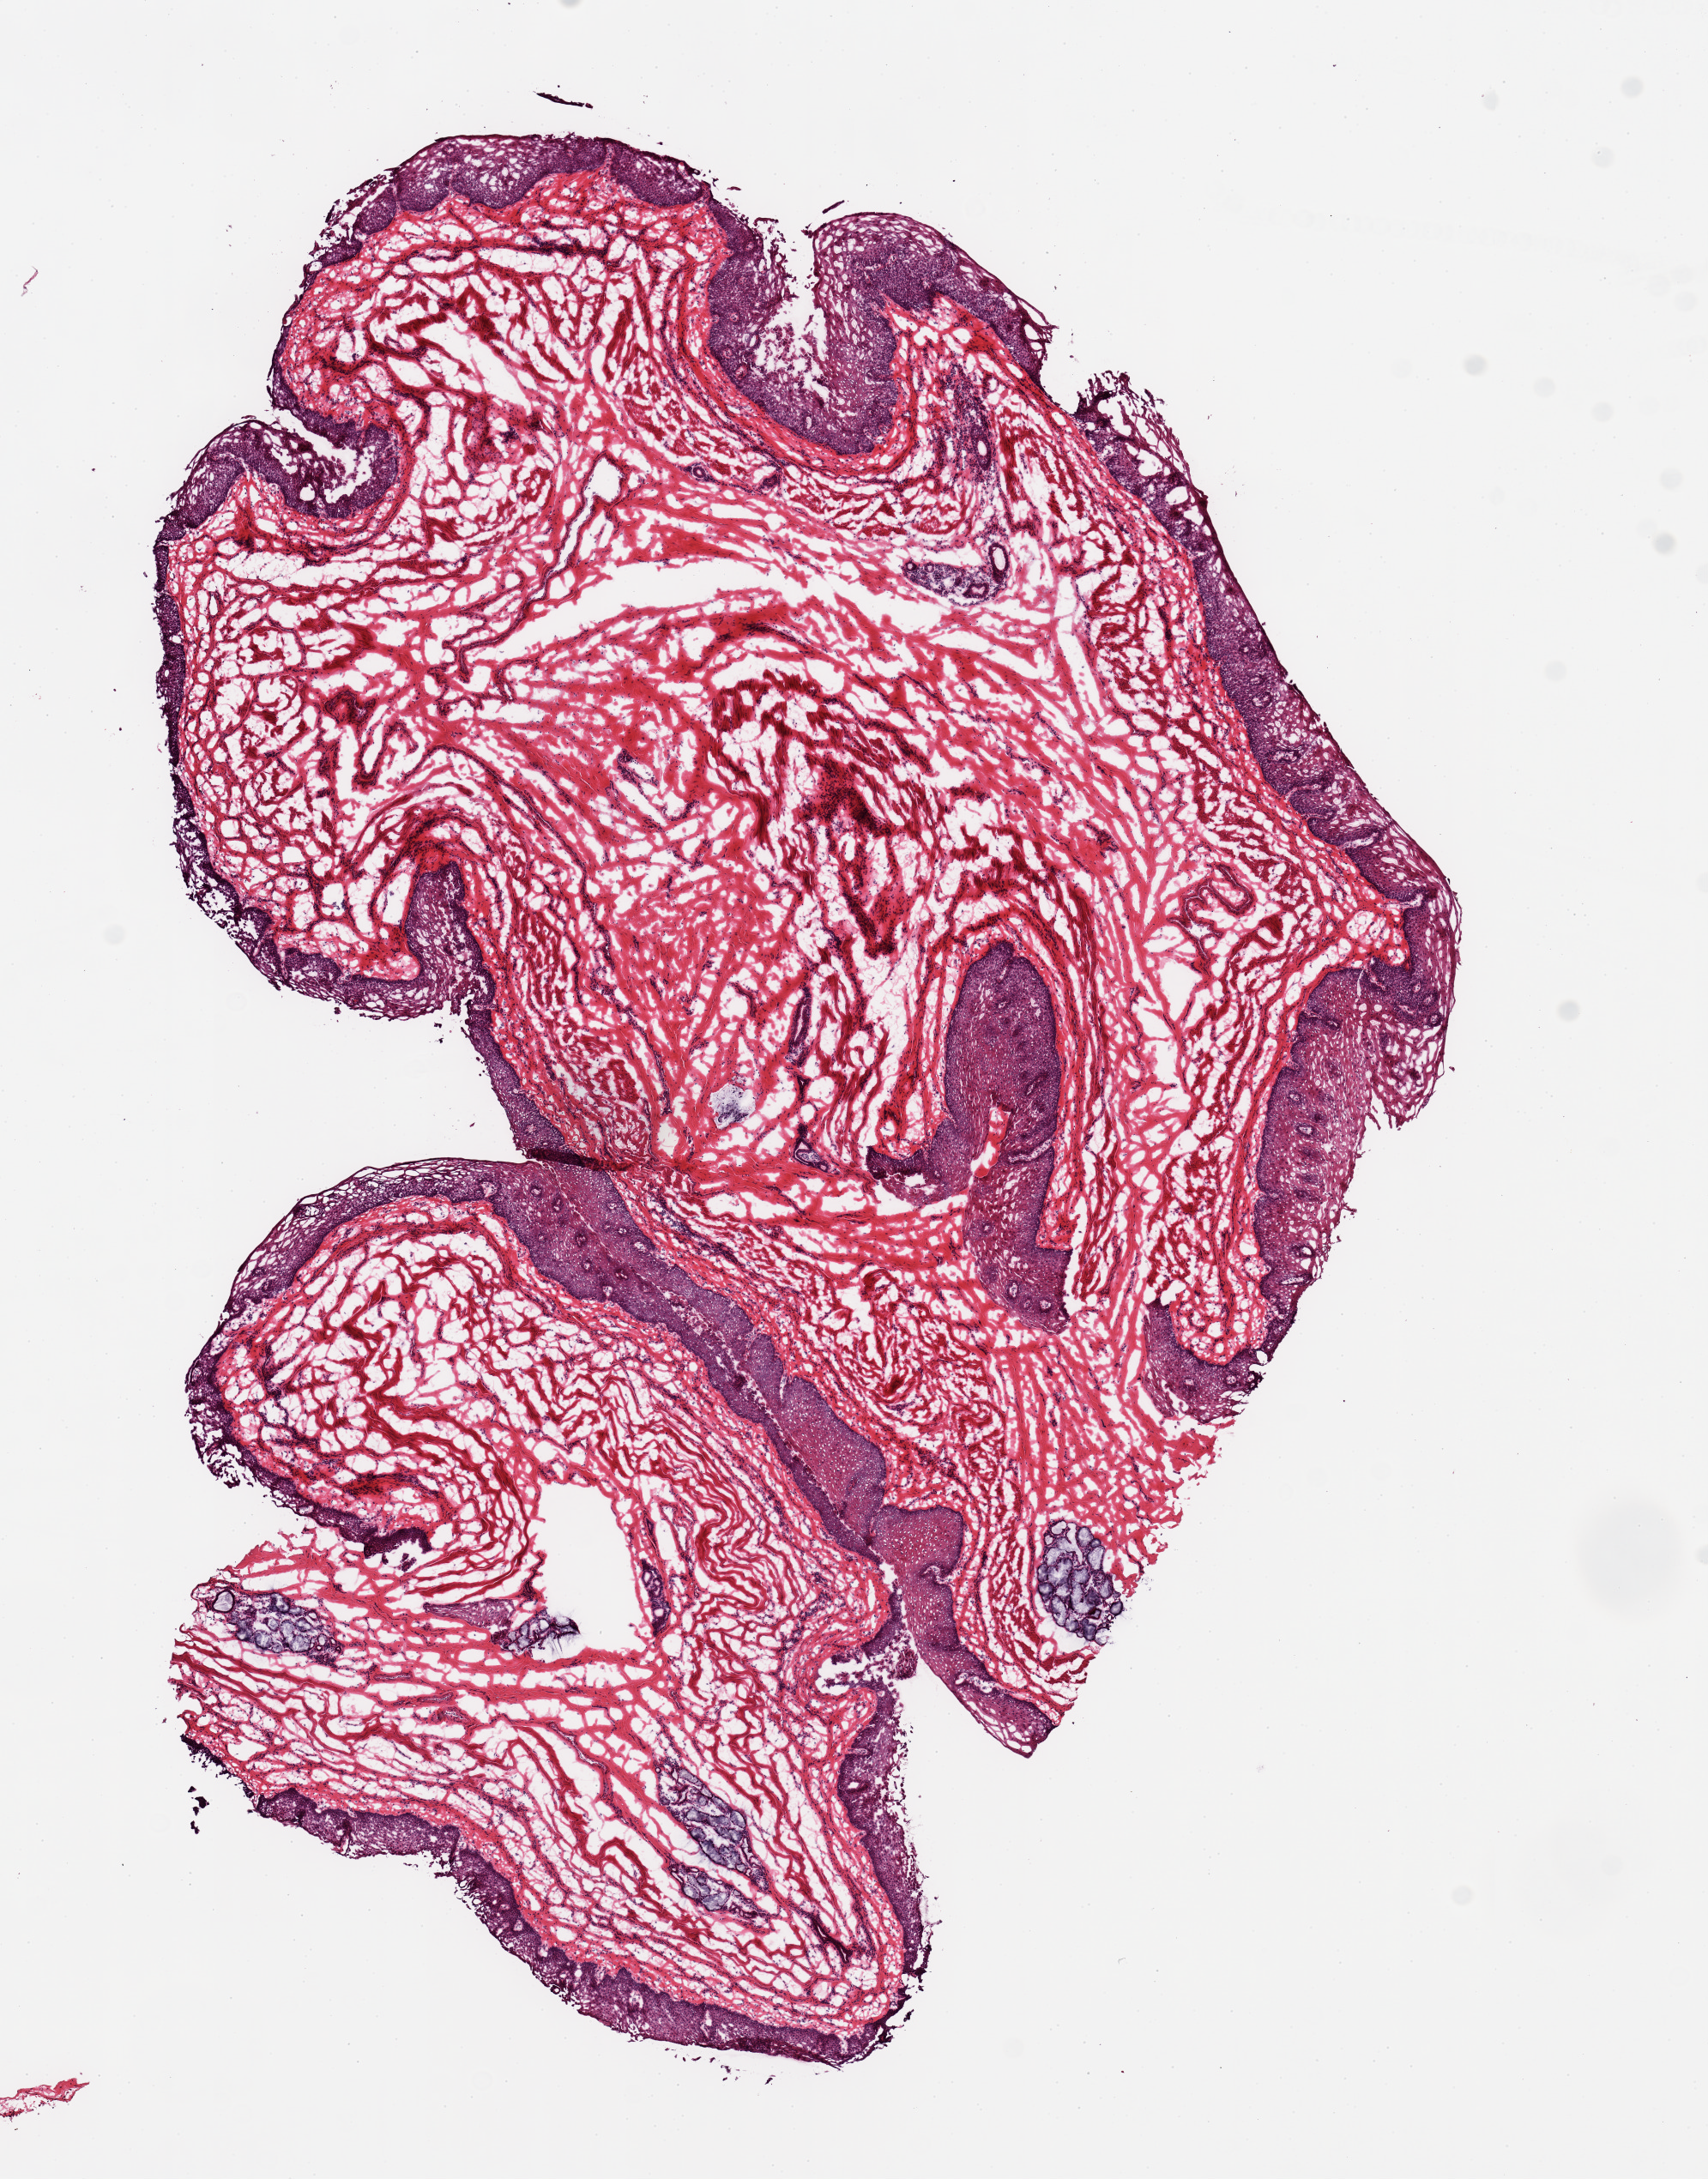
Whole-slide image, hematoxylin and eosin (H&E) stain, brightfield, a low-resolution overview of the entire scanned area, about 7.9 x 10.0 mm, frozen section (dry ice), target tissue: esophageal mucous membrane, donor tissue sample. Donor: female.
* review note (as recorded): 1 piece; includes few clusters of submucosal glands